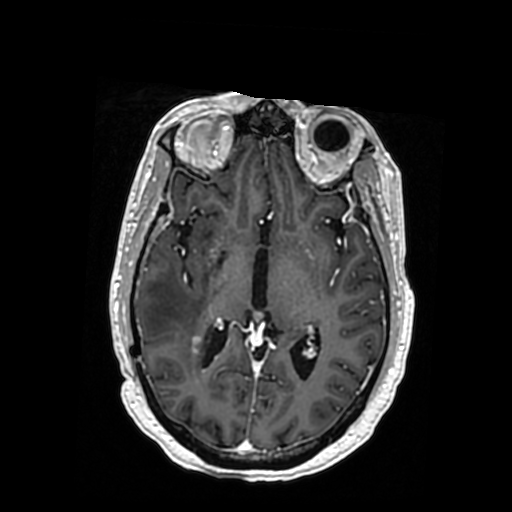
Brain MRI from a brain-tumour surgery series, one axial slice. Position 191 of 364 along the scan axis. T1-weighted post-contrast. 0.5 mm slice thickness. 512 × 512 image matrix, field of view 260 × 260 mm. Case-level facts recorded for this patient, not image findings: histopathology: Oligodendroglioma; WHO grade: 3; IDH mutation: yes; tumour location: Right Posterior Temporal Inferior Parietal.
Structures marked on this image (expert manual segmentation):
- previous resection cavity: bounding box <218,256,223,265> (left, top, right, bottom; pixels)
- tumour: <148,334,154,347>